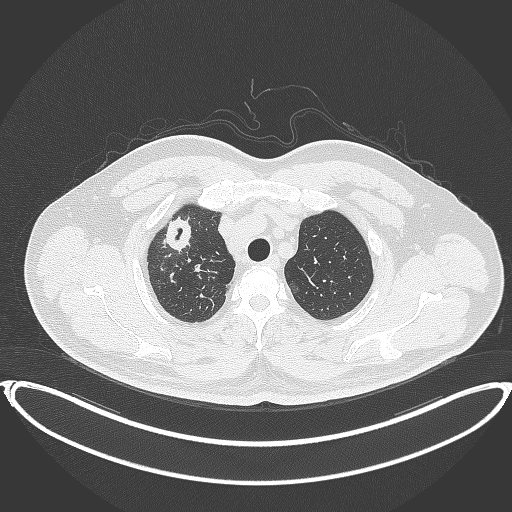
Chest CT, one axial slice; slice 329 of 399 in the series (ordered by position); reconstruction kernel B70f; 120 kVp; lung window (W 1500 / L -600 HU); 512 × 512 image matrix, field of view 445 × 445 mm. Male patient, age 53 years. Case-level facts recorded for this patient, not image findings: clinical TNM (as recorded): T2a N0 M0.
Structures marked on this image (bounding box drawn by a radiologist):
- lung tumour (recorded histology: adenocarcinoma): bounding box [x1, y1, x2, y2] px = [162, 210, 197, 256]